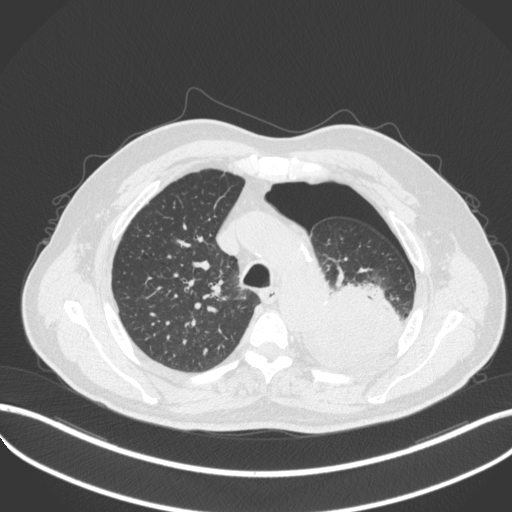
Chest CT, one axial slice; slice 379 of 466 in the series (ordered by position); reconstruction kernel B31f; lung window (W 1500 / L -600 HU); 1 mm slice thickness; 512 × 512 image matrix. Patient: male, 76 years. From the clinical record (not read from this slice): clinical TNM (as recorded): T3 N0 M1b.
Structures marked on this image (bounding box drawn by a radiologist):
- lung tumour (recorded histology: adenocarcinoma): bounding box (x1, y1, x2, y2) in pixels: (292, 278, 399, 374)